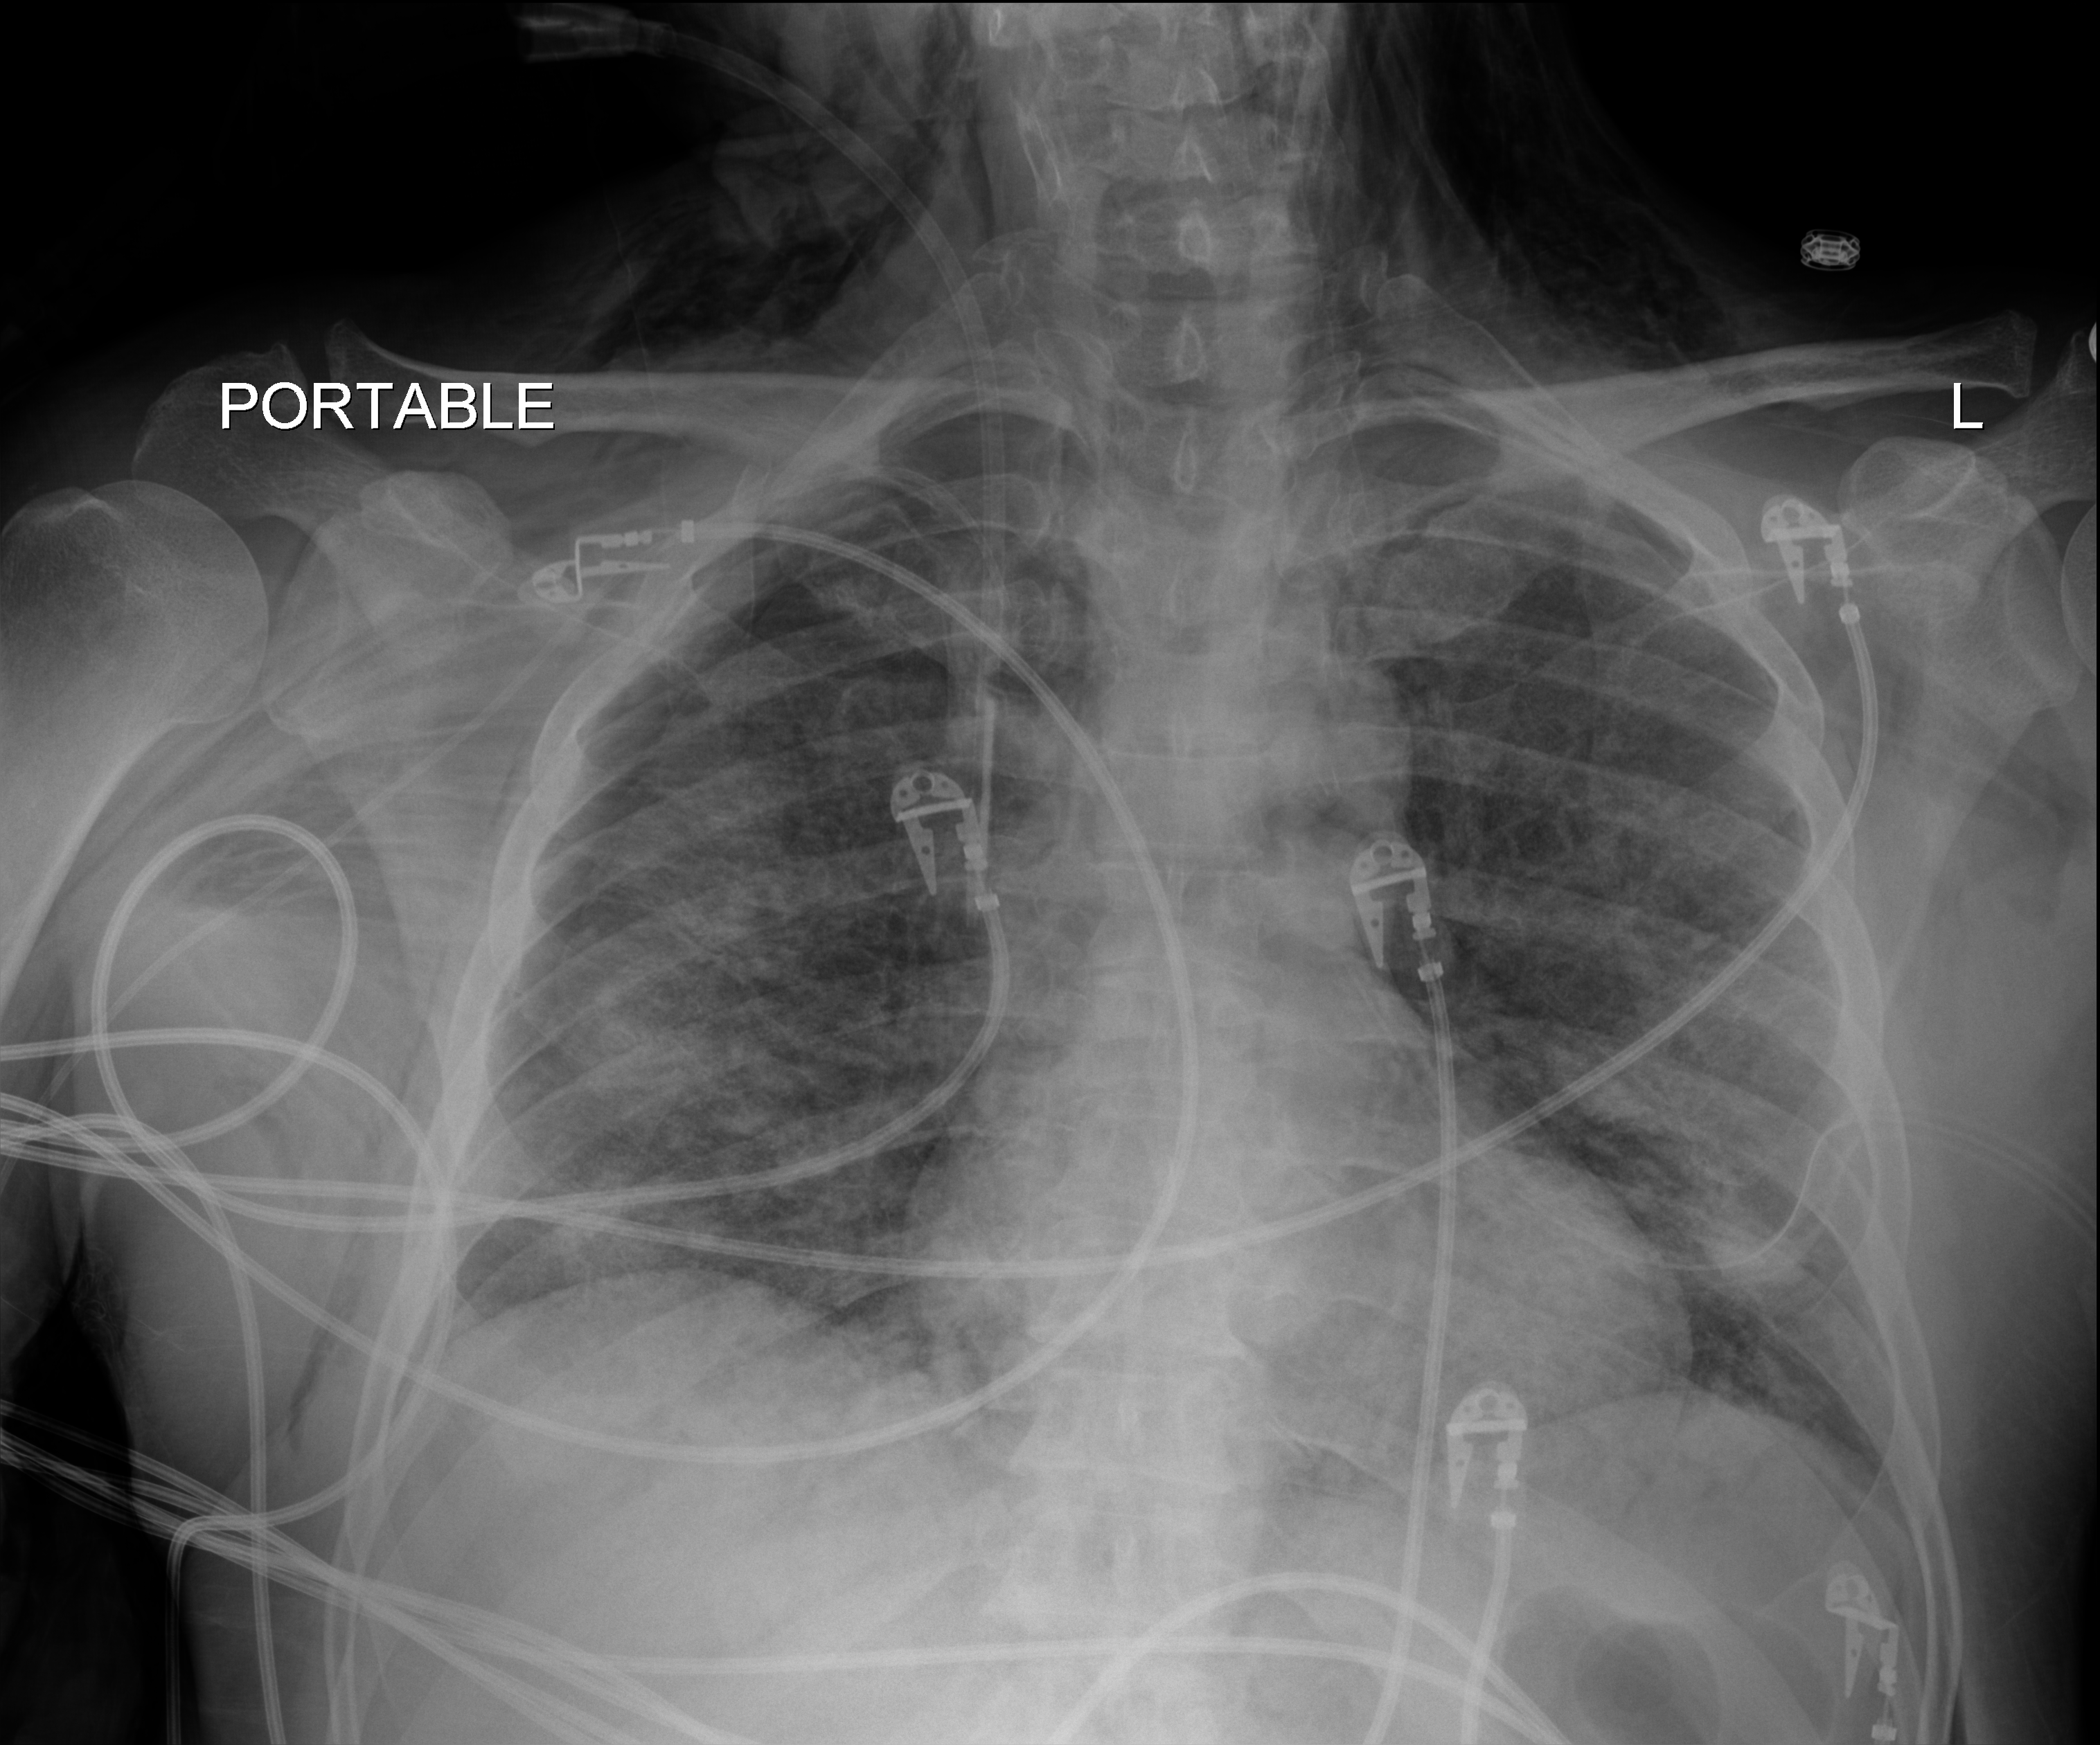
Chest radiograph (digital radiography), anteroposterior (AP) projection. Male patient hospitalised with COVID-19, age 18–59 years.
Hospital-stay facts (about this admission, not read from this image; timing relative to this image not recorded): other chronic lung disease (admission record): no; chronic kidney disease (admission record): no.